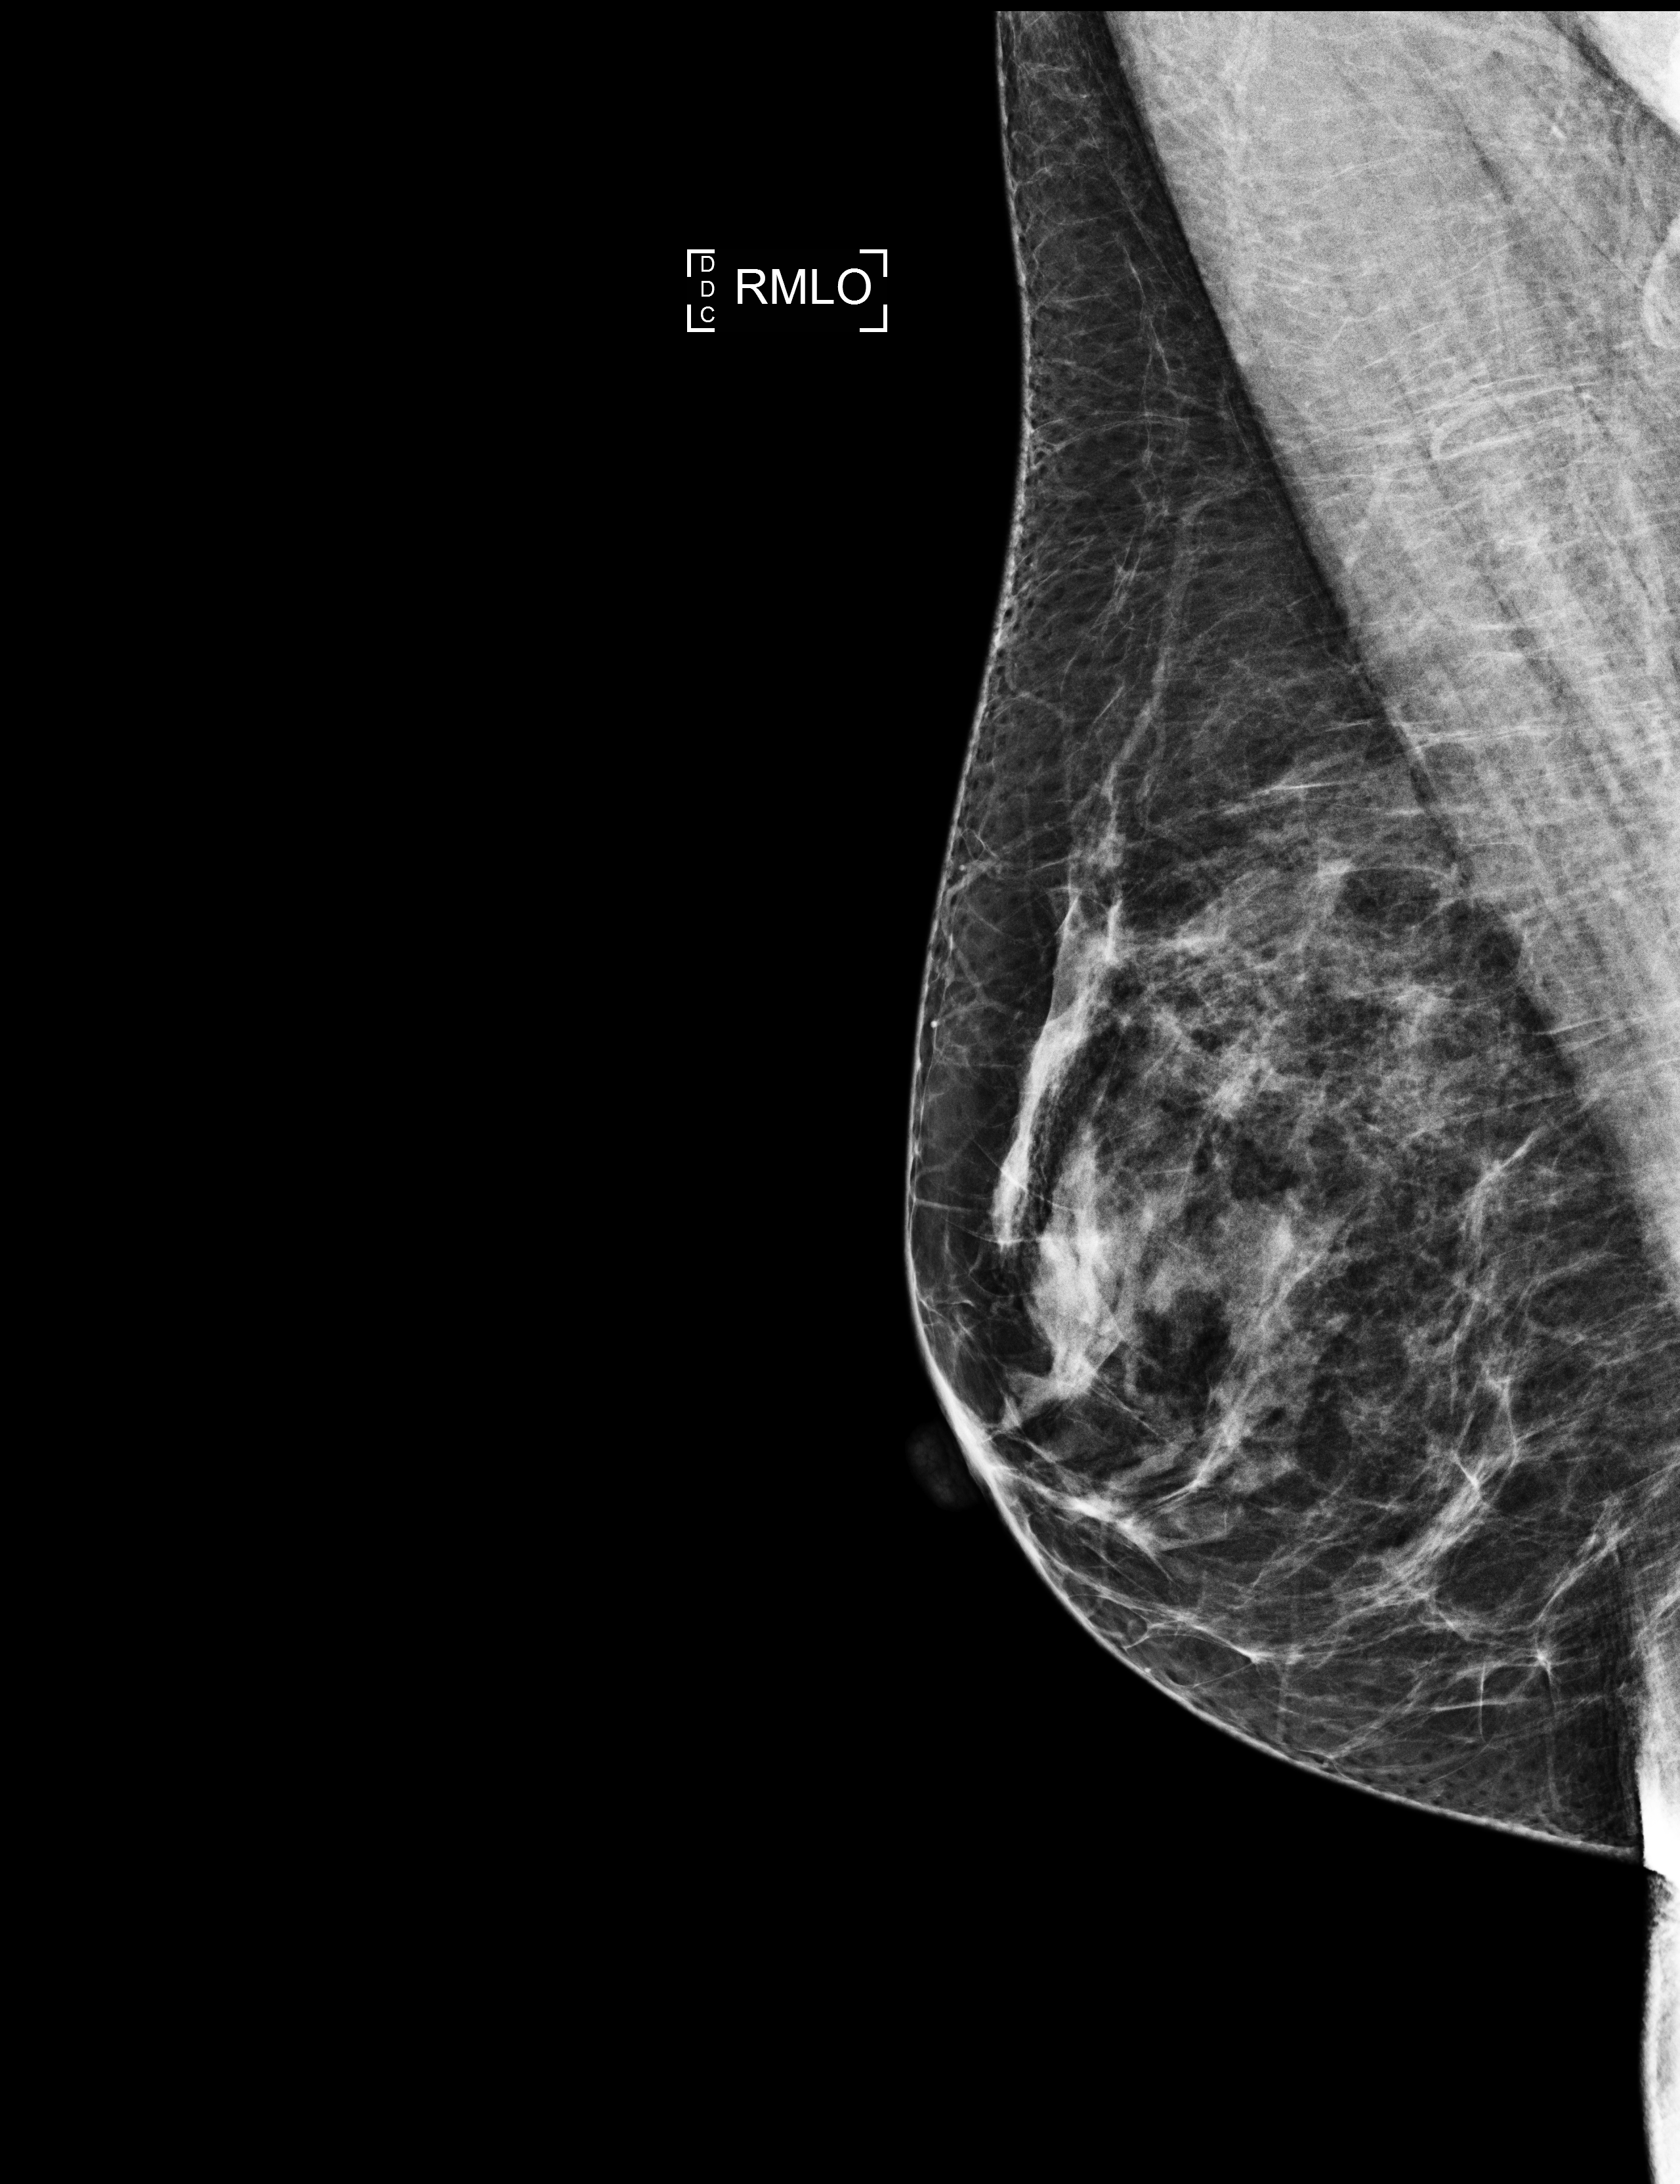
Digital mammogram (FFDM); right breast; medio-lateral oblique projection; screening examination. Female patient, age 59 years.
Breast density at the screening exam (both breasts): heterogeneously dense (BI-RADS density category c). Final BI-RADS category for the screening round (tomosynthesis exam, both breasts): category 2. Recall: no recall after this screen.